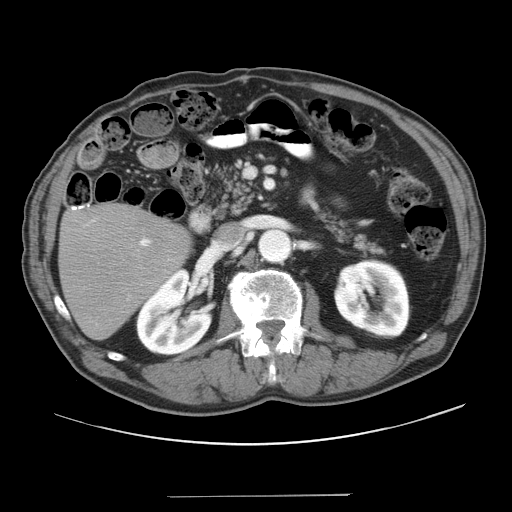
Contrast-enhanced abdominal CT, one axial slice; position 16 of 41 along the scan axis; reconstruction kernel STANDARD; 120 kVp; intravenous contrast given; soft-tissue window (W 400 / L 40 HU); 5 mm slice thickness; 512 × 512 image matrix. Male patient, age 75 years. From the clinical record (not read from this slice): diagnosis: colorectal cancer liver metastases, imaged before liver resection; multiple liver metastases: no.
Outlined on this slice (outlined manually by an expert reader):
- liver: bounding box (x1, y1, x2, y2) in pixels: (60, 206, 191, 339)
- planned liver remnant (the part of the liver to remain after resection): (60, 206, 191, 339)
- portal vein (with intrahepatic branches): (139, 237, 170, 260)